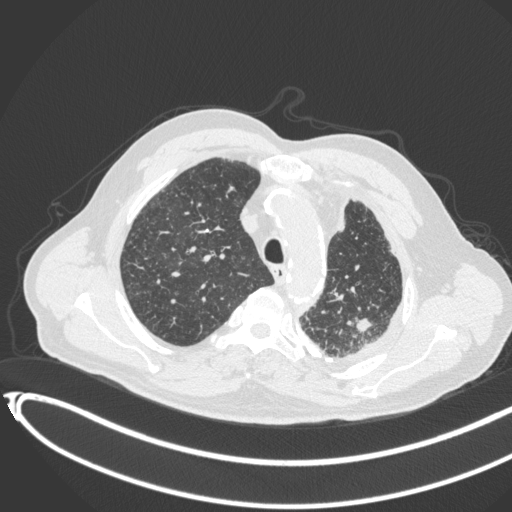
Chest CT, one axial slice. Slice 335 of 451 in the series (ordered by position). 120 kVp. Lung window (W 1500 / L -600 HU). 1 mm slice thickness. 512 × 512 image matrix, field of view 400 × 400 mm. Patient: male, 78 years. From the clinical record (not read from this slice): clinical TNM (as recorded): T1c N0 M1.
Annotated regions visible in this slice (rectangle marked by the reading radiologist):
- lung tumour (recorded histology: adenocarcinoma): bounding box [x1, y1, x2, y2] px = [355, 311, 383, 339]